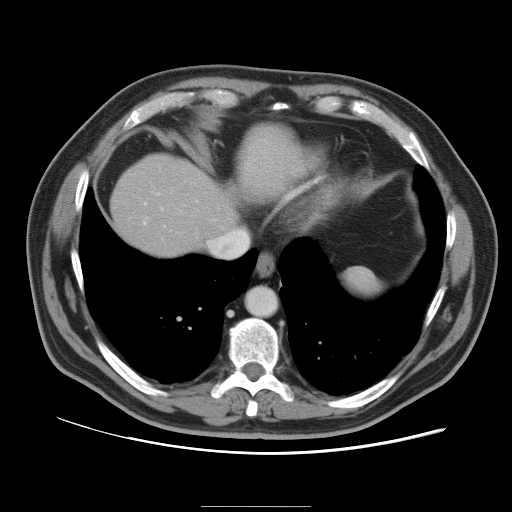
Contrast-enhanced abdominal CT, one axial slice; slice 89 of 105 in the series (ordered by position); 120 kVp; soft-tissue window (W 400 / L 40 HU); 5 mm slice thickness; 512 × 512 image matrix. Male patient, age 64 years. From the clinical record (not read from this slice): diagnosis: colorectal cancer liver metastases, imaged before liver resection; multiple liver metastases: yes; largest metastasis: 3 cm; chemotherapy before resection: yes.
Annotated regions visible in this slice (outlined manually by an expert reader):
- hepatic veins: bounding box (x1, y1, x2, y2) in pixels: (143, 222, 146, 224)
- liver: (113, 155, 236, 255)
- planned liver remnant (the part of the liver to remain after resection): (113, 159, 224, 254)